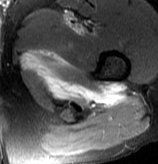
MRI of an extremity soft-tissue mass, one axial slice; slice 70 of 70 in the series (ordered by position); T2-weighted fat-saturated; MR volume resampled by the dataset authors to the PET/CT grid (not the native acquisition matrix); 158 × 164 image matrix, field of view 154 × 160 mm. Male patient. Case-level facts recorded for this patient, not image findings: histological type: extraskeletal osteosarcoma; grade: high; site of the primary tumour: left adductur.
Structures marked on this image (expert contour drawn on MRI and transferred to this co-registered scan by the dataset authors):
- gross tumour volume (mass): bounding box (x1, y1, x2, y2) in pixels: (47, 12, 126, 108)